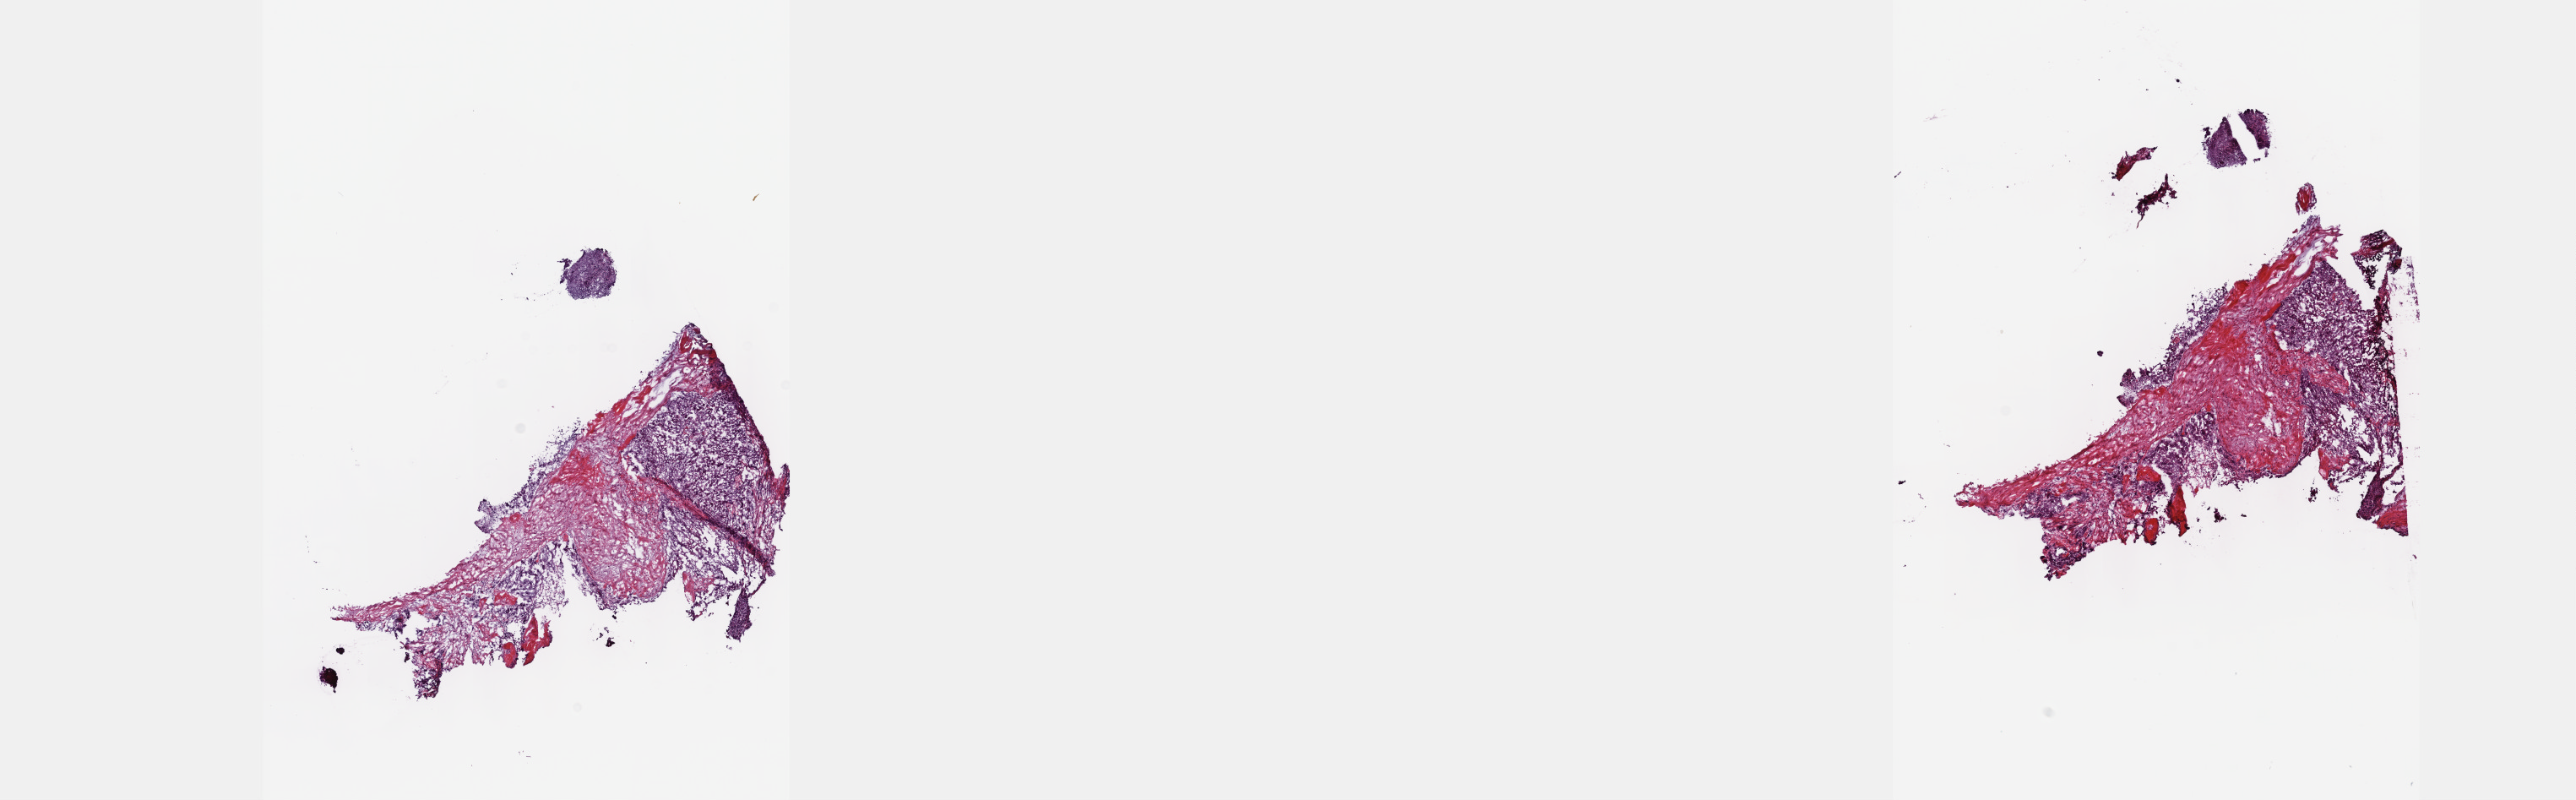
Whole-slide histology image, H&E — shown as a low-resolution overview of the whole scanned area (about 24.6 x 7.7 mm, acquisition: 40x scan), frozen section, sample: primary tumour, liver. Patient: male, age at initial diagnosis 34 years. Histologic grade: G3 (poorly differentiated). Composition of this section per pathologist review: tumour cells 65%, tumour nuclei 65%, normal cells 0%, stromal cells 35%, necrosis 0%. Infiltration values recorded for this section: lymphocyte infiltration 3%, monocyte infiltration 1%, neutrophil infiltration 1%.
TNM: T1 N0 MX. Histologic diagnosis: Hepatocellular carcinoma, fibrolamellar. AJCC pathologic stage: I (7th edition).